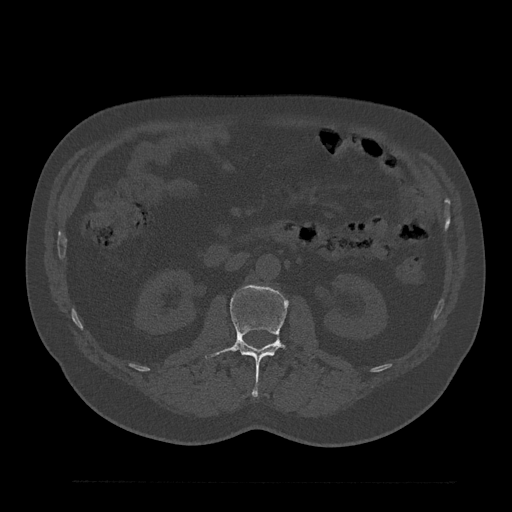
CT including the spine, one axial slice; position 97 of 797 along the scan axis; bone window (W 1800 / L 400 HU); 0.5 mm slice thickness; 512 × 512 image matrix, field of view 430 × 430 mm. Patient: male, 61 years. Case-level facts recorded for this patient, not image findings: primary cancer: prostate.
Outlined on this slice (semi-automatic segmentation, software-assisted and operator-edited):
- L2 vertebra: bounding box (x1, y1, x2, y2) in pixels: (204, 285, 315, 396)